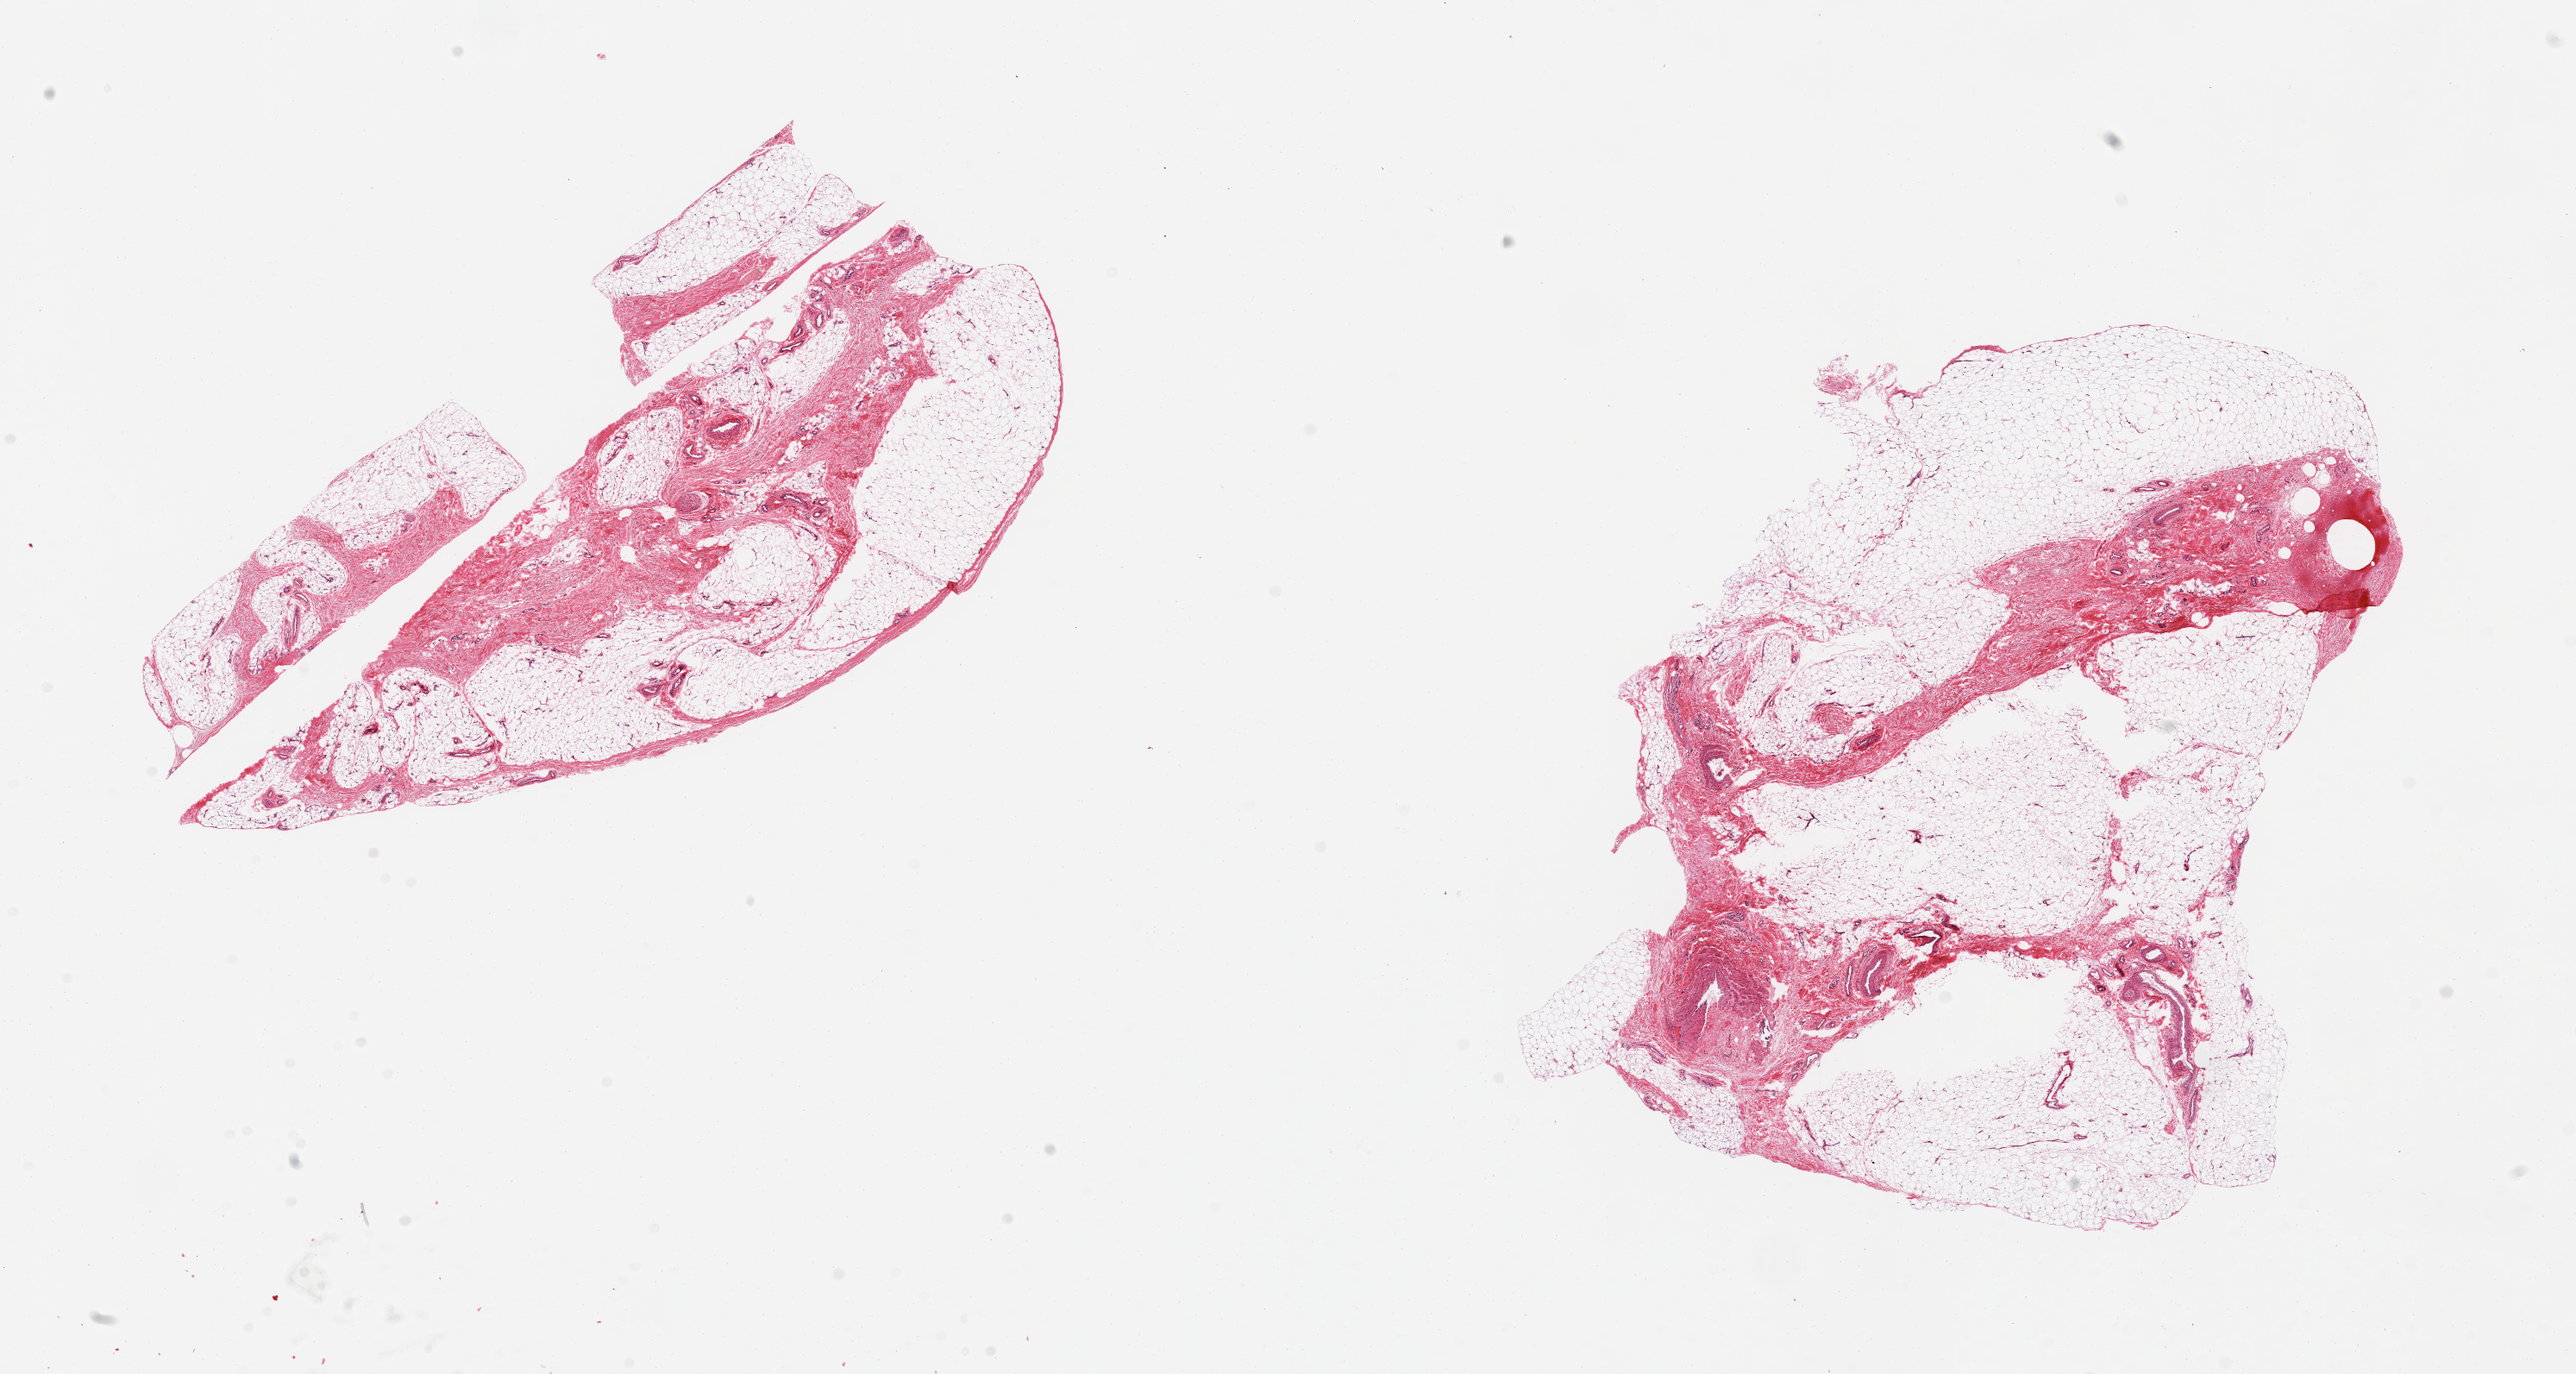
Whole-slide image, haematoxylin and eosin stain — low-resolution overview of the scanned area, about 23.6 x 12.6 mm; PAXgene-fixed, paraffin-embedded tissue; target tissue: adipose tissue; donor tissue sample. Donor sex: male.
Review note (as recorded): 2 pieces, ~20 and 30% fibrous with few larger vessels.